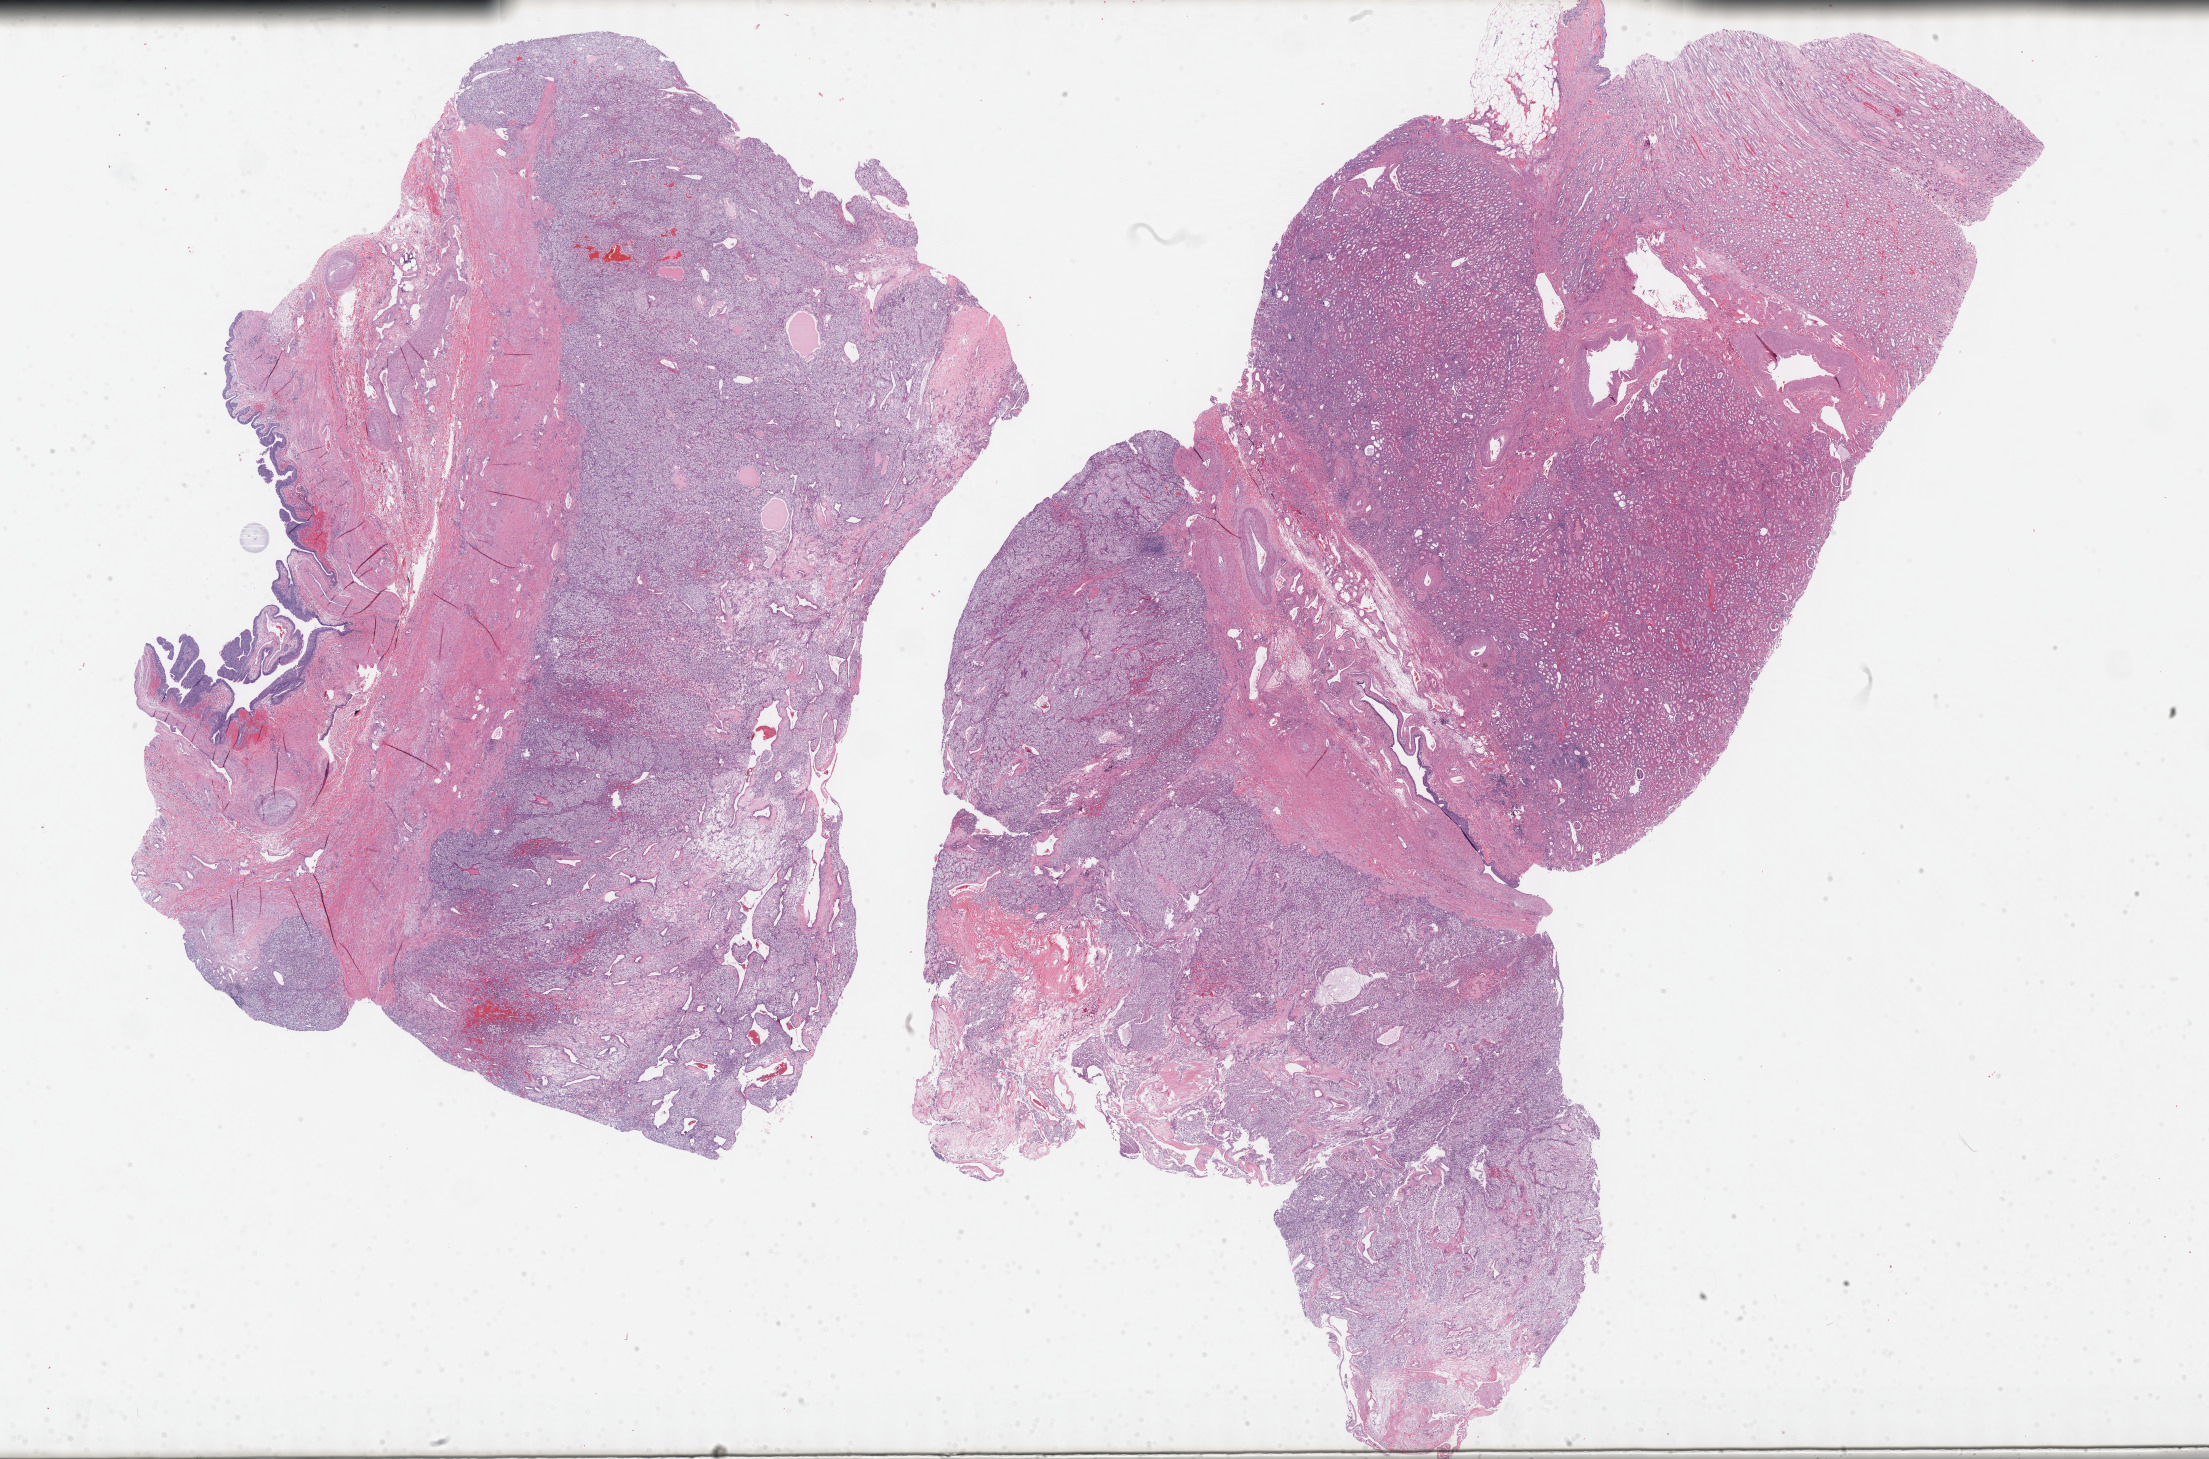
Whole-slide histology image, Hematoxylin and eosin (H&E) stained, whole scanned area (about 35.7 x 23.6 mm, acquisition: 40x scan) shown as a low-resolution overview; formalin-fixed paraffin-embedded (FFPE) diagnostic section; sample: primary tumour, kidney. Patient: male, age at initial diagnosis 68 years. Histologic grade: G2 (moderately differentiated).
- TNM: T2a NX MX
- histologic diagnosis: Clear cell adenocarcinoma, NOS
- AJCC pathologic stage: II (7th edition)